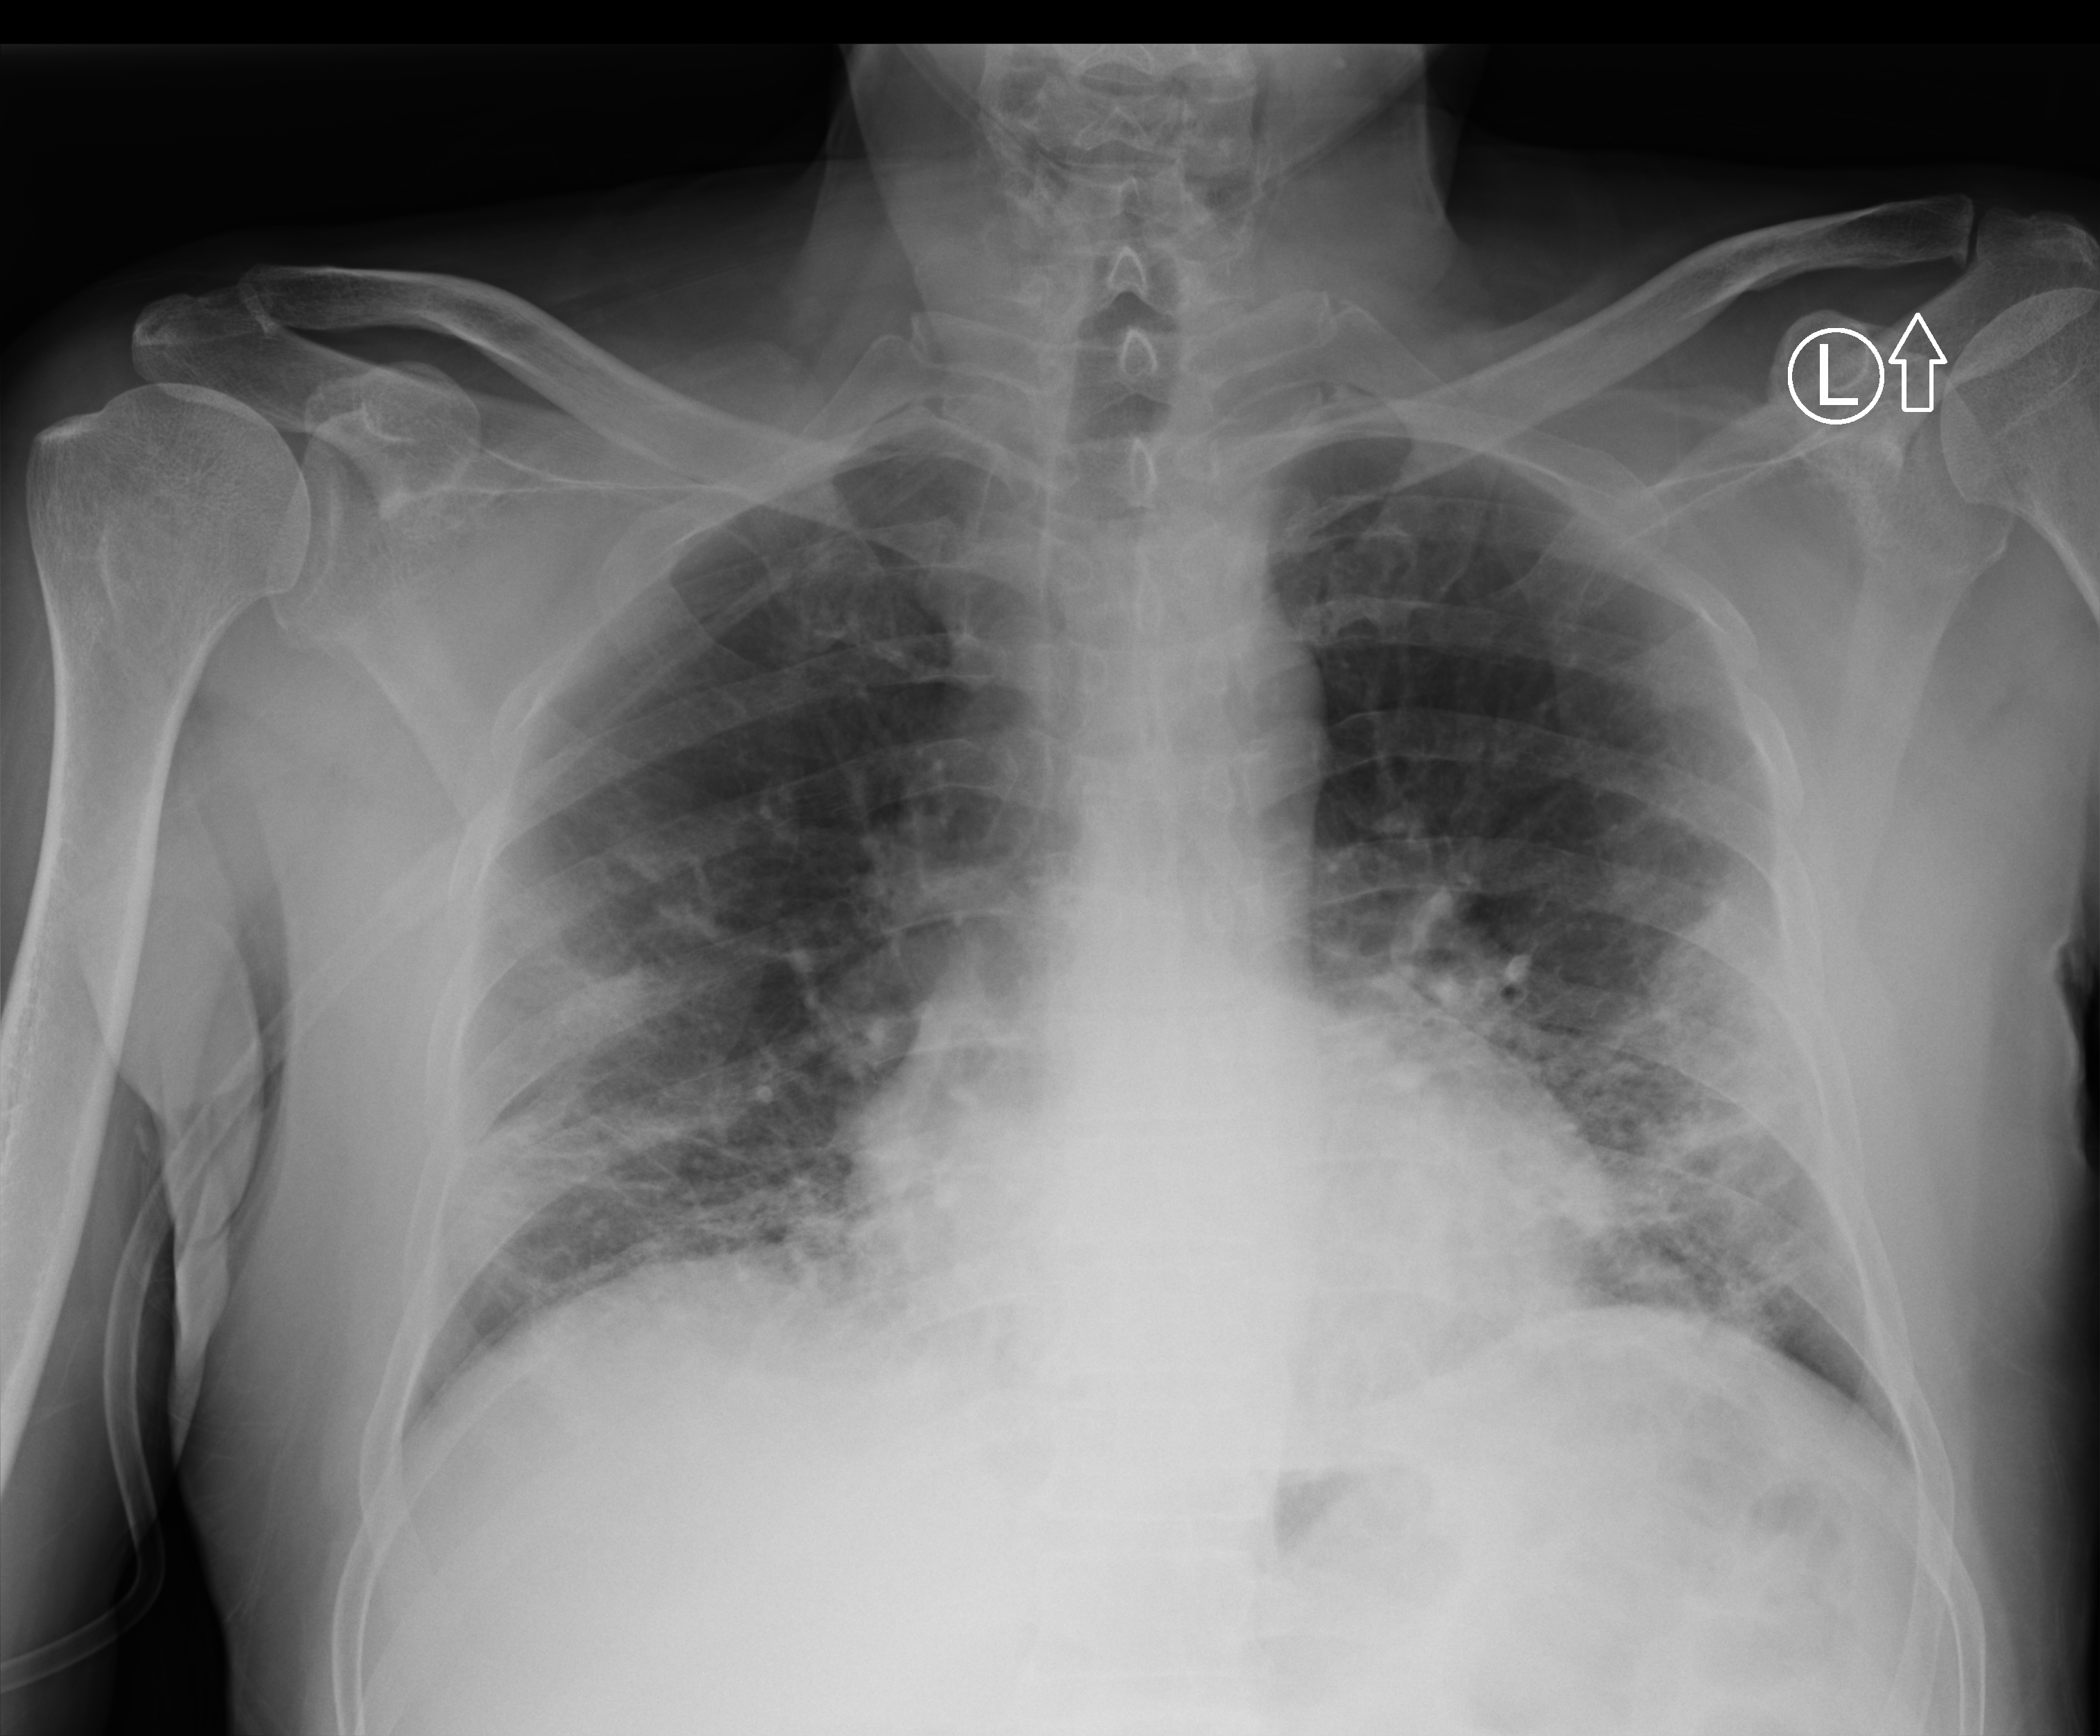
Bedside chest radiograph (computed radiography), anteroposterior (AP) projection. Patient hospitalised with COVID-19; male, aged 18–59 years.
Admission-level facts for this patient (not findings on this image; timing relative to this image not recorded): mechanically ventilated during this hospital stay: no.